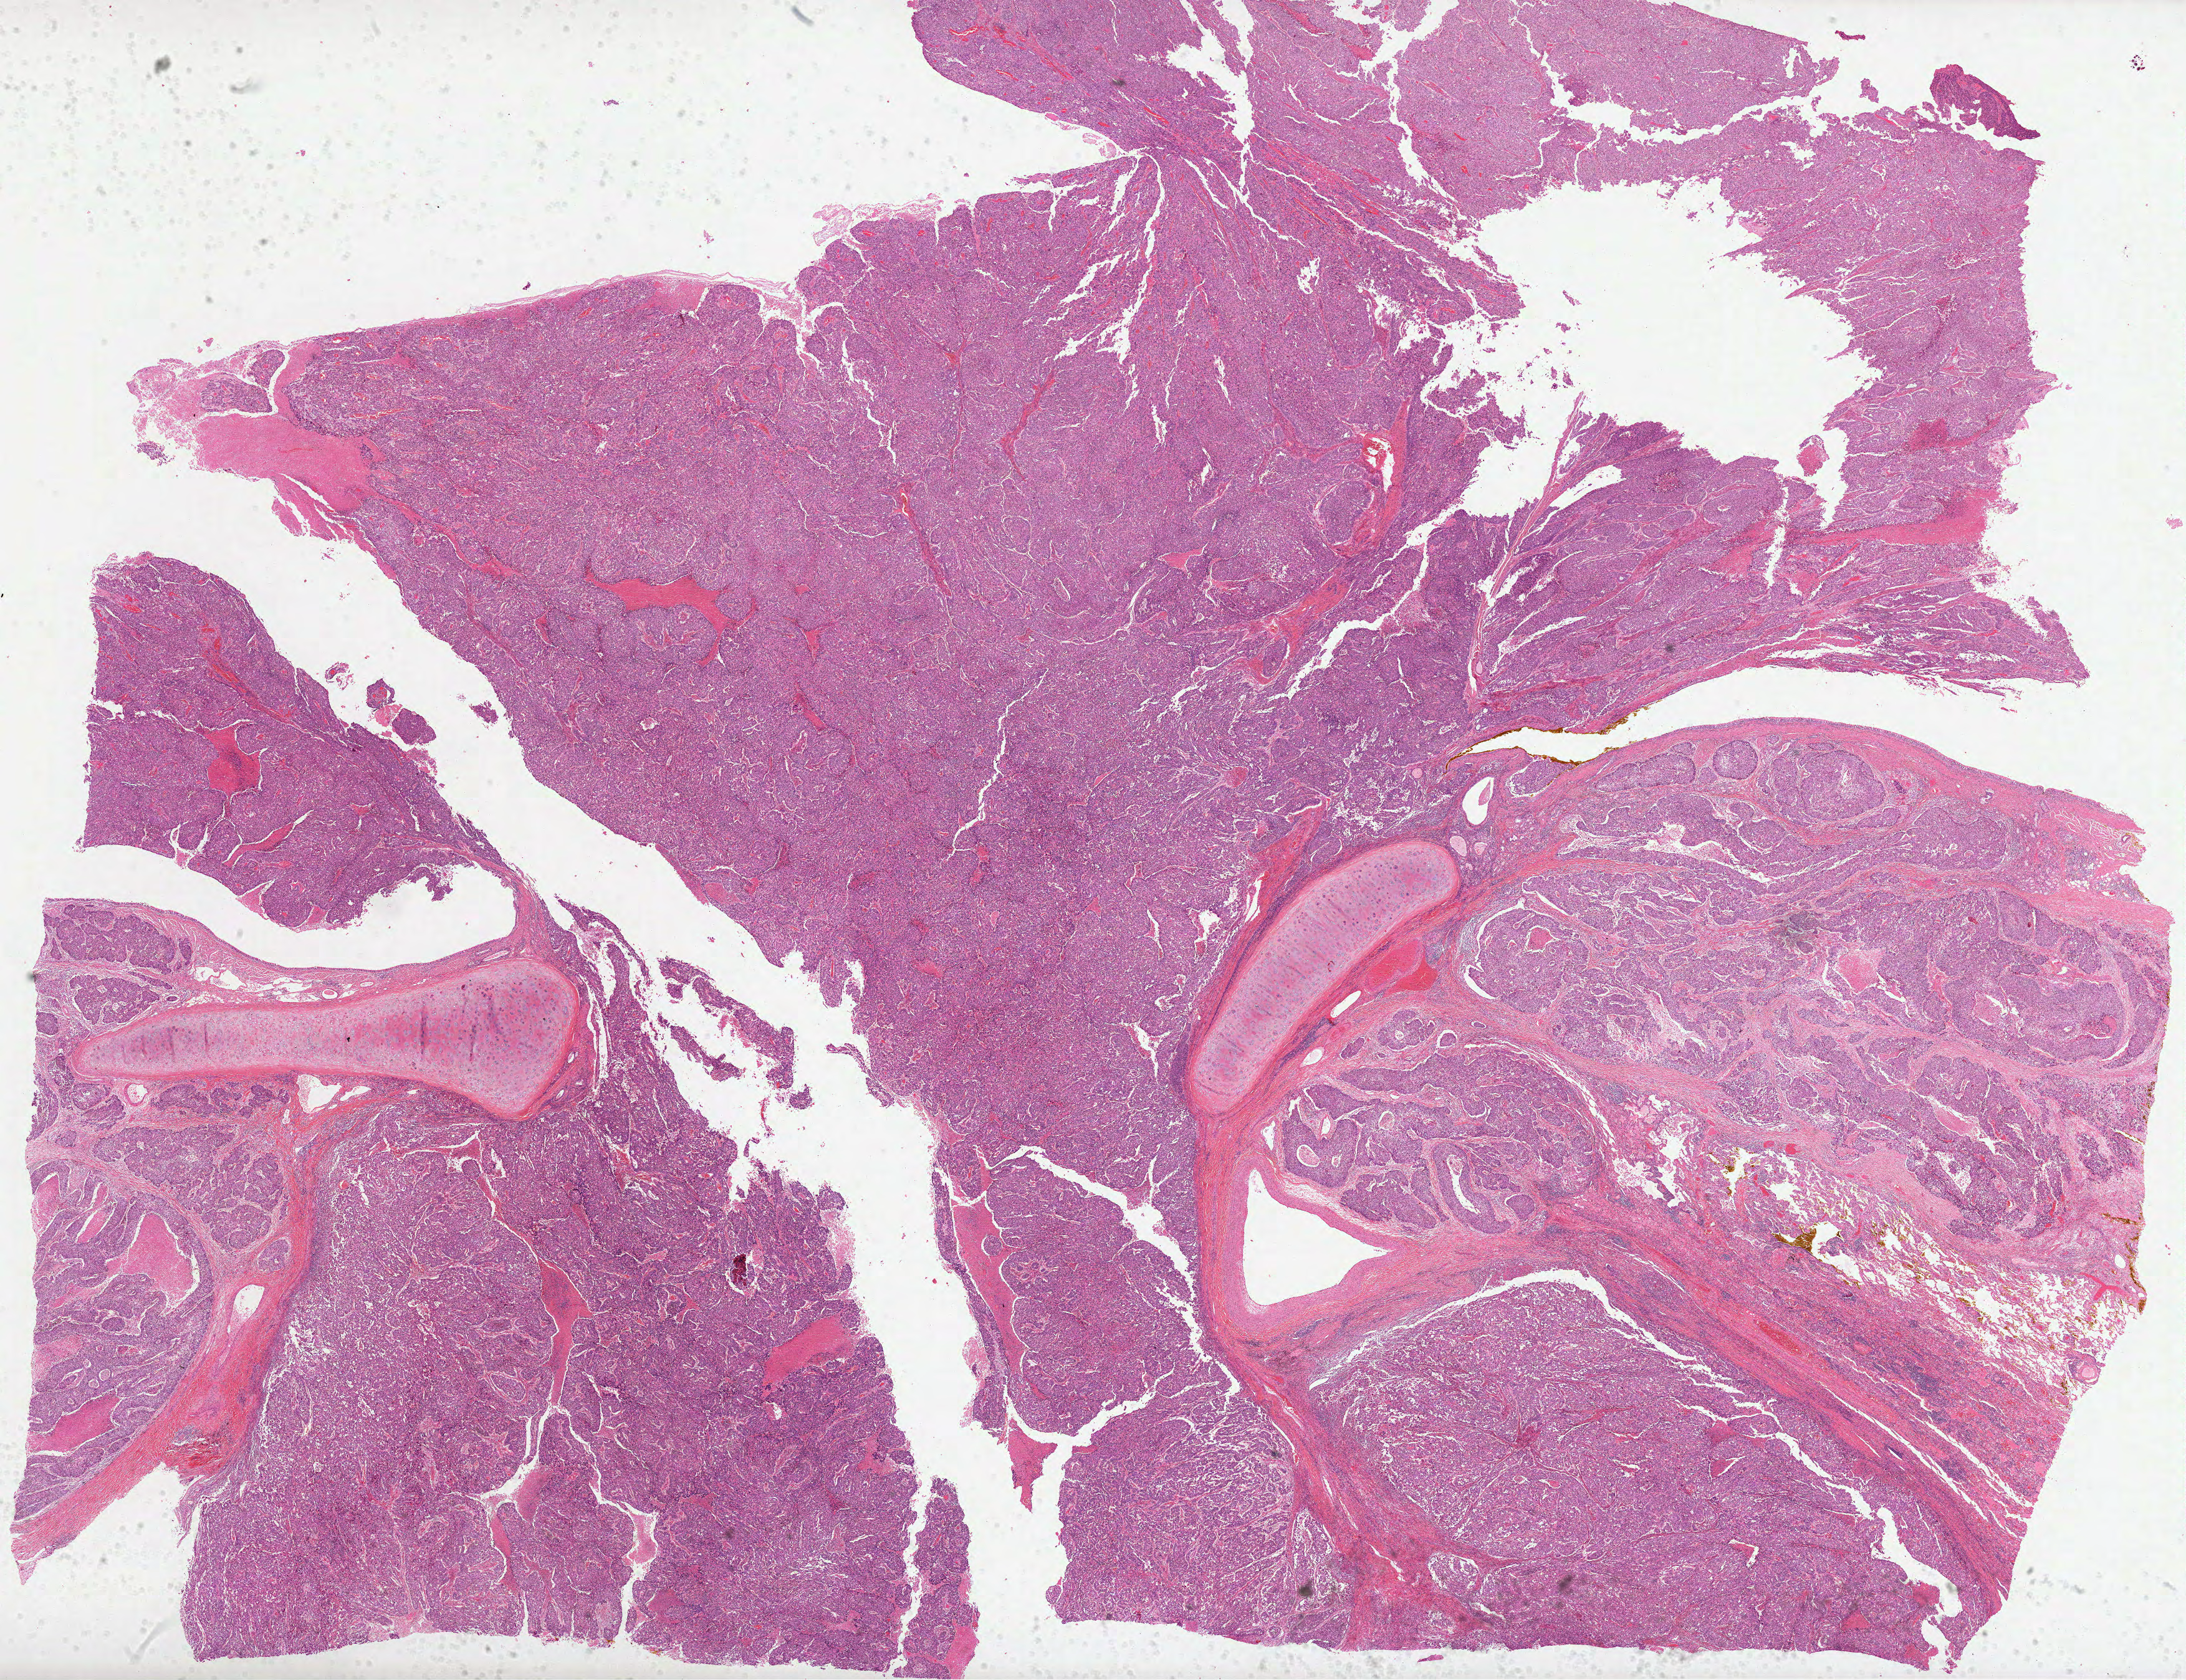
H&E-stained whole-slide image, low-resolution overview of the scanned area, about 28.3 x 21.7 mm (slide scanned at 40x); FFPE section; sample: primary tumour, lung. Patient: male, age at initial diagnosis 68 years.
- AJCC pathologic stage: IIB (6th edition)
- pathologic diagnosis: Squamous cell carcinoma, NOS